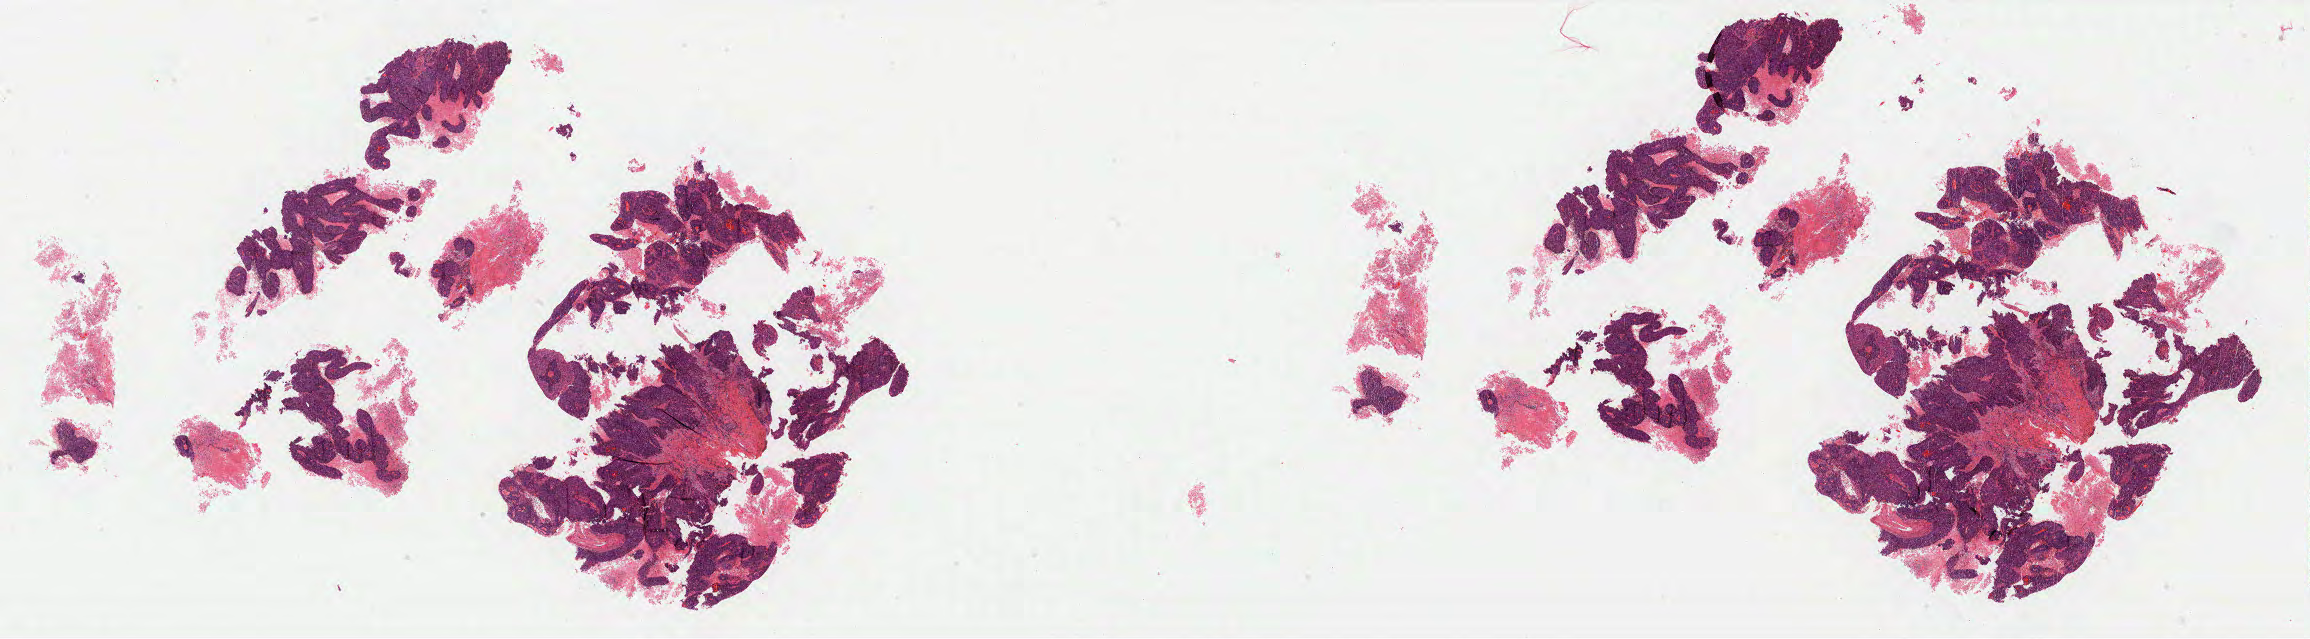
Whole-slide histology image, H&E — low-resolution overview of the scanned area, about 37.0 x 10.2 mm (acquisition: 40x scan); FFPE section; sample: primary tumour, cervix. Female, age 54 years at initial diagnosis. Histologic grade: G2 (moderately differentiated).
• histologic diagnosis: Squamous cell carcinoma, NOS (cervix uteri)
• FIGO stage: IB1
• lymph nodes positive (case pathology): 3 of 39 examined